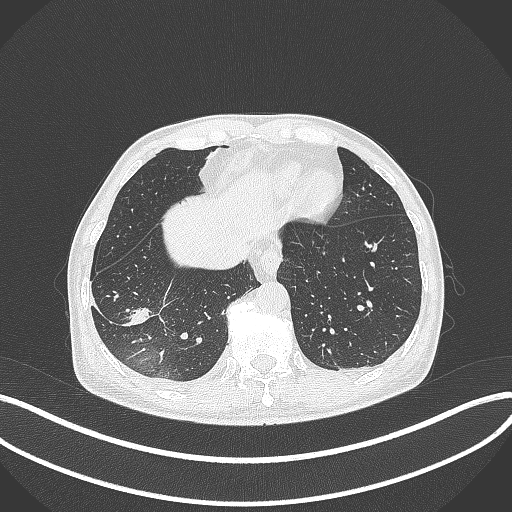
Chest CT, one axial slice. Position 87 of 388 along the scan axis. Reconstruction kernel B70f. 120 kVp. Lung window (W 1500 / L -600 HU). 512 × 512 image matrix, field of view 400 × 400 mm. Male patient, age 64 years. Case-level facts recorded for this patient, not image findings: clinical TNM (as recorded): T3 N0 M0.
Outlined on this slice (bounding box drawn by a radiologist):
- lung tumour (recorded histology: adenocarcinoma): box from (x=119, y=301) to (x=155, y=328) px